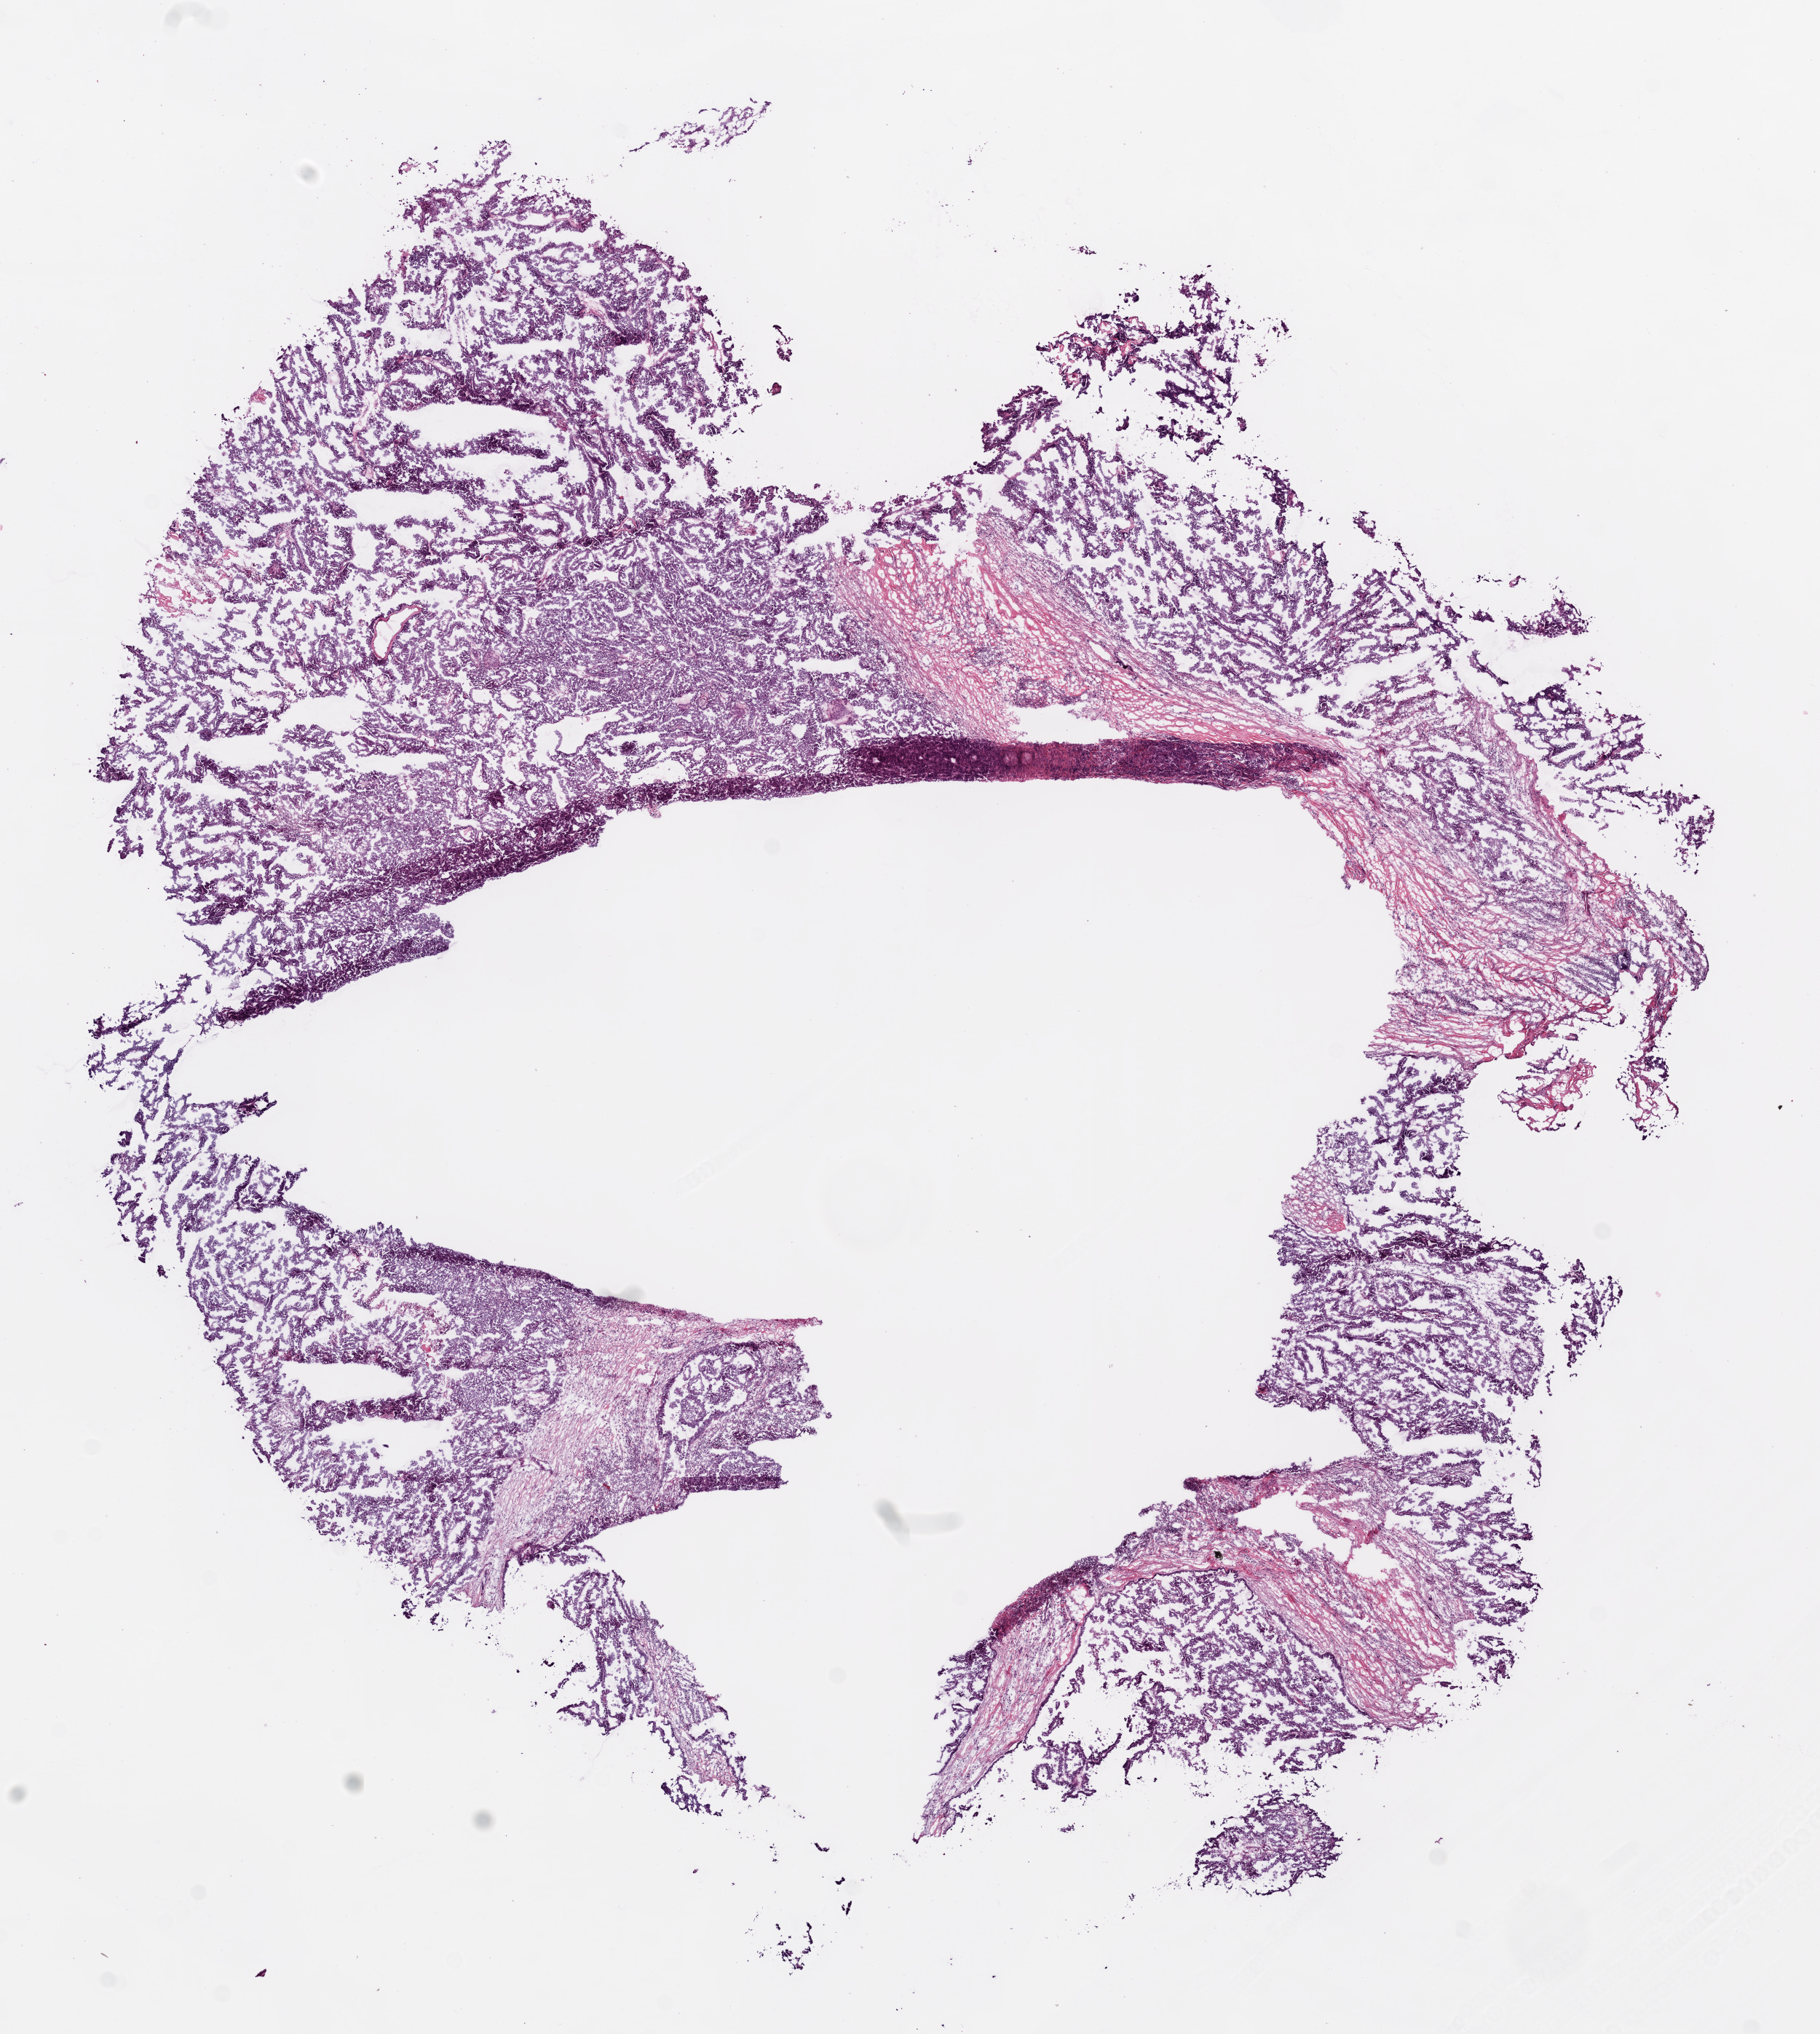
Hematoxylin and eosin (H&E) stained whole-slide image, a low-resolution overview of the entire scanned area, about 10.0 x 11.2 mm (from a 20x scan), frozen section, ovary, recurrent tumour sample. Female, age 75 years at initial diagnosis. Pathologist review of this section (percent, as recorded): tumour cells 80%, tumour nuclei 90%, normal cells 0%, stromal cells 20%, necrosis 0%.
• this section: recurrent tumour
• patient diagnosis: Serous cystadenocarcinoma, NOS